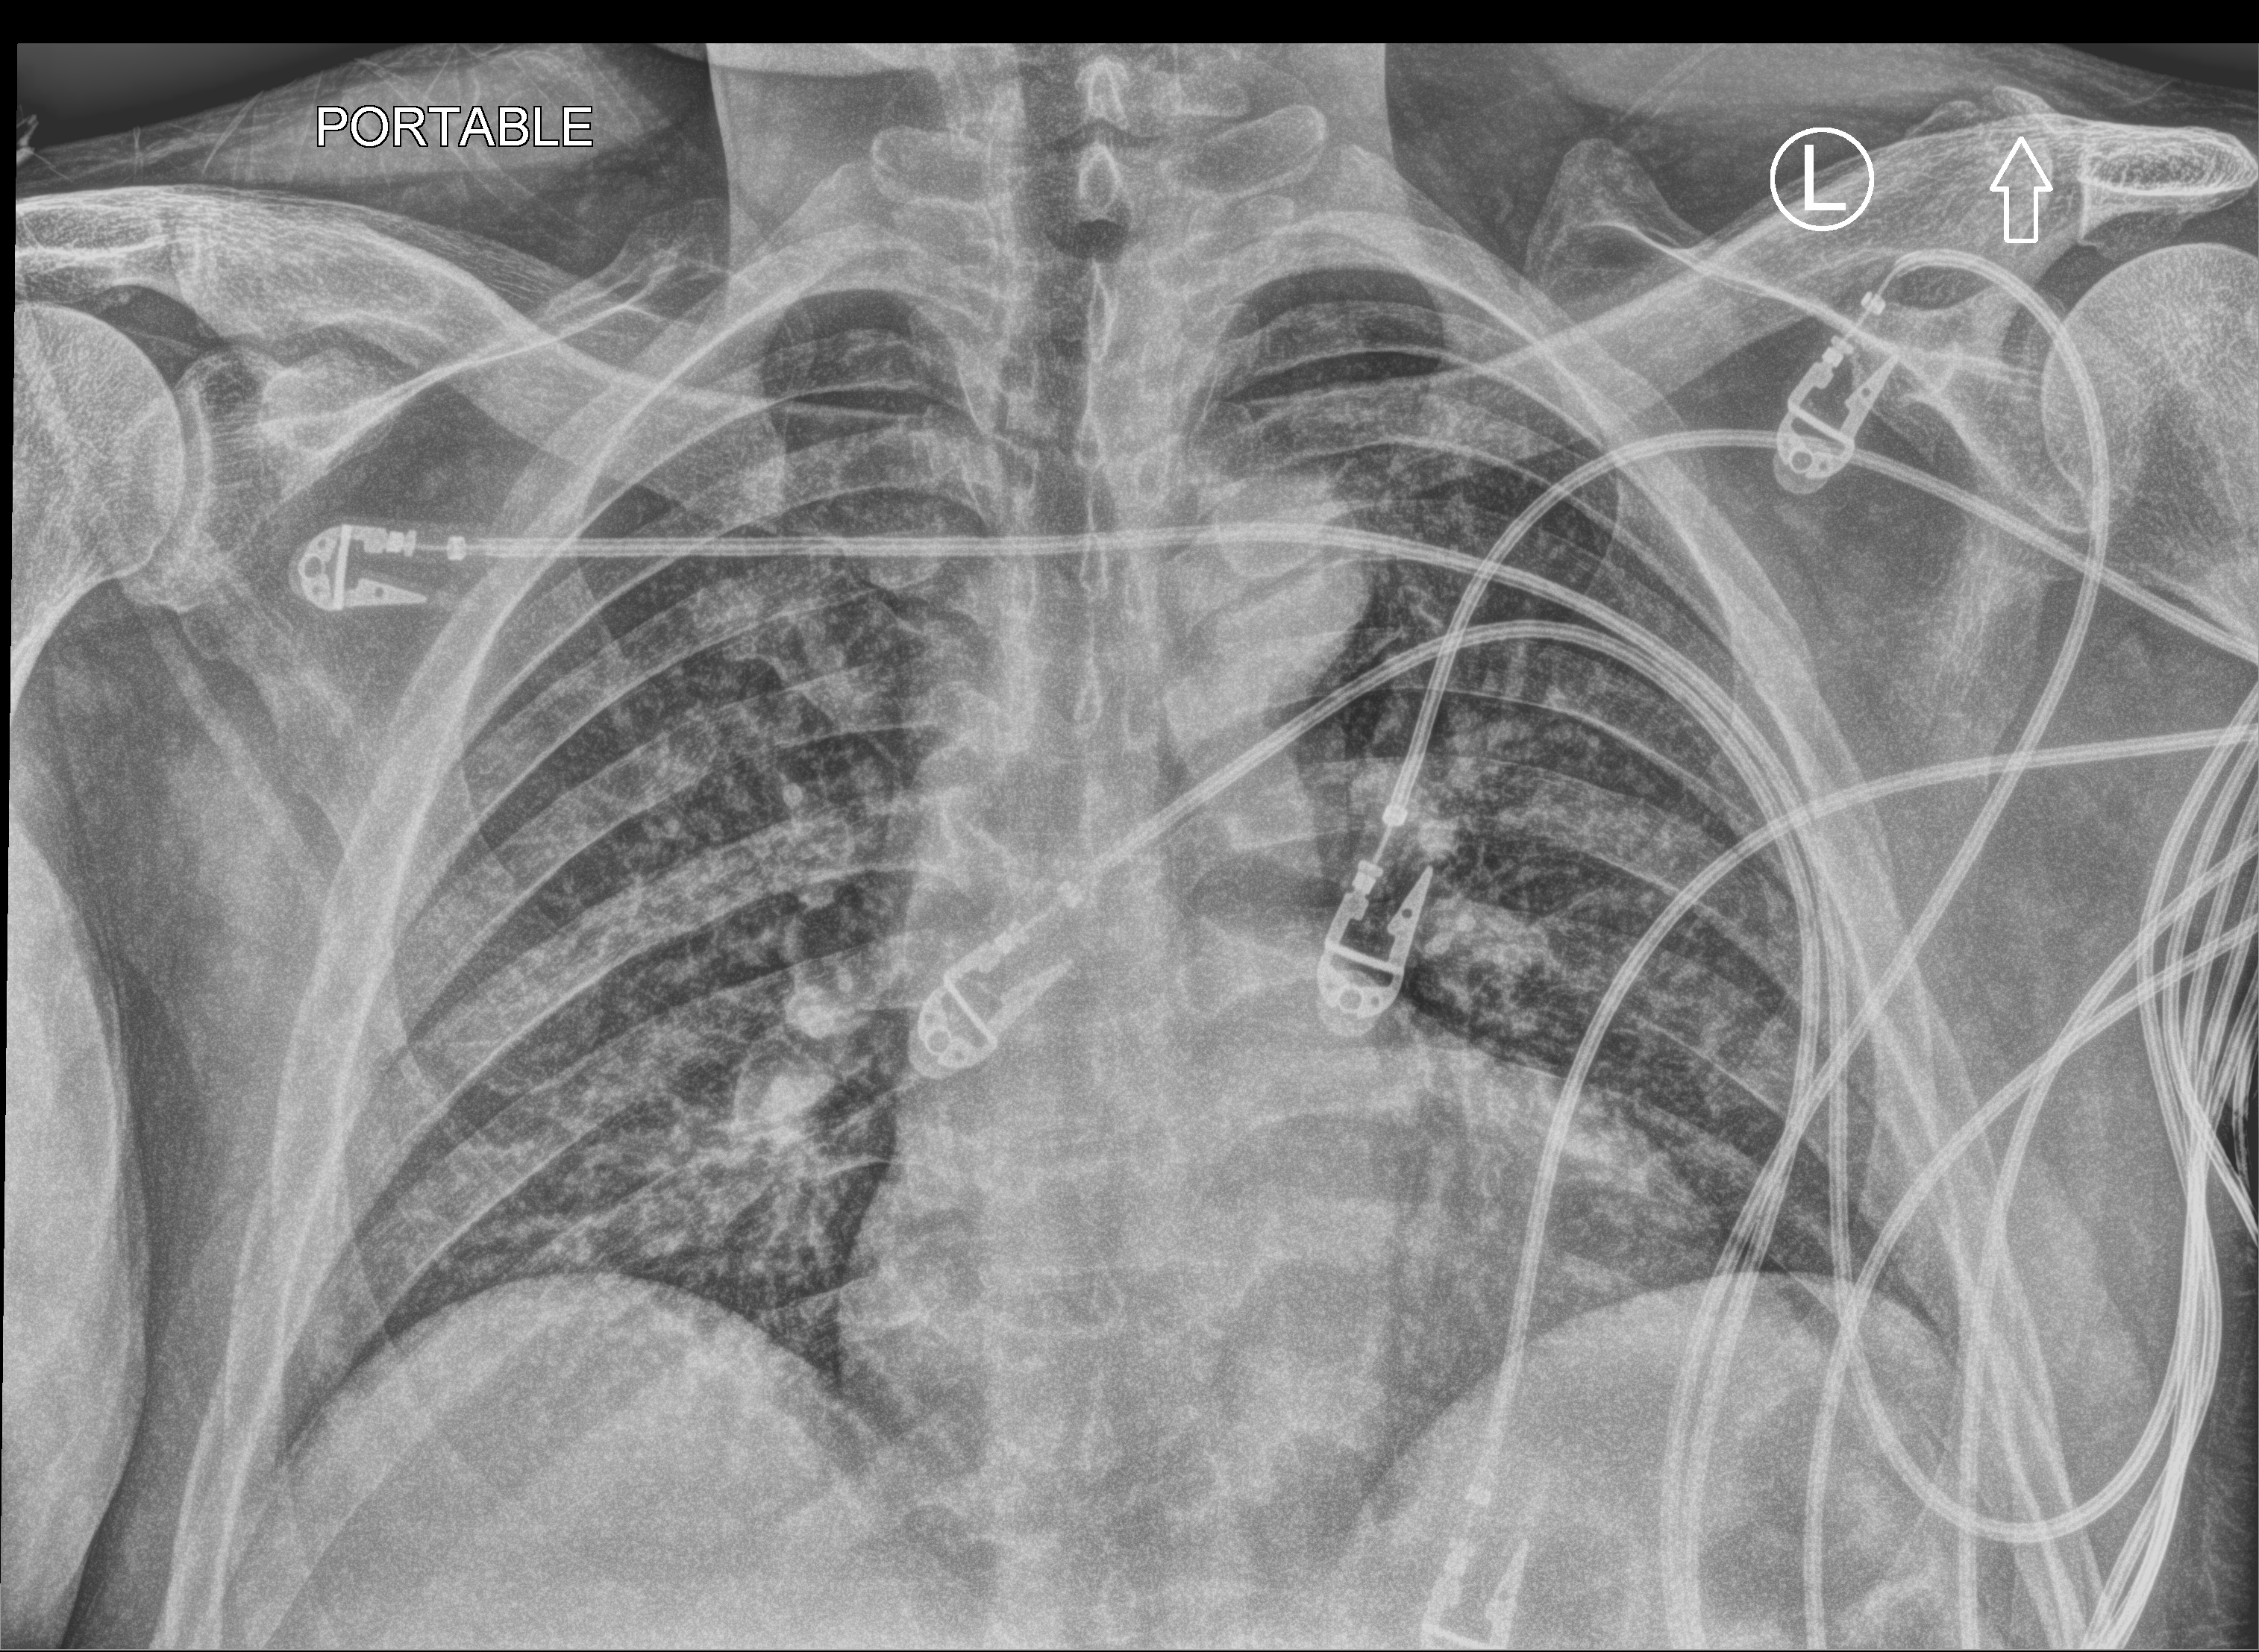
Chest X-ray (portable). Male patient hospitalised with COVID-19, age 18–59 years.
Hospital-stay facts (about this admission, not read from this image; timing relative to this image not recorded):
- length of hospital stay: 2 days
- admitted to intensive care during this hospital stay: no